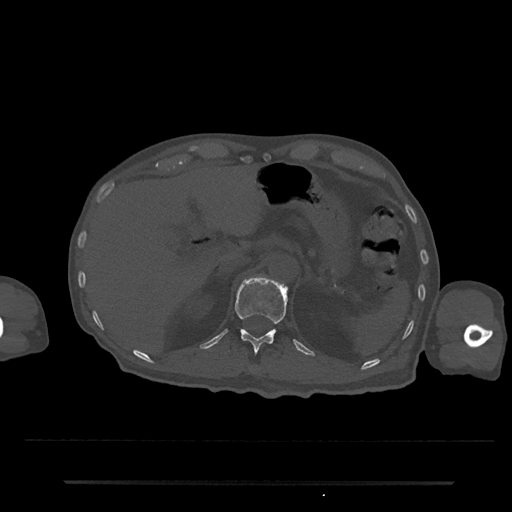
CT including the spine, one axial slice; slice 190 of 797 in the series (ordered by position); bone window (W 1800 / L 400 HU); 0.5 mm slice thickness; 512 × 512 image matrix. Male patient, age 74 years. Case-level facts recorded for this patient, not image findings: primary cancer: prostate.
Outlined on this slice (semi-automatic segmentation, software-assisted and operator-edited):
- T12 vertebra: box from (x=235, y=278) to (x=288, y=353) px